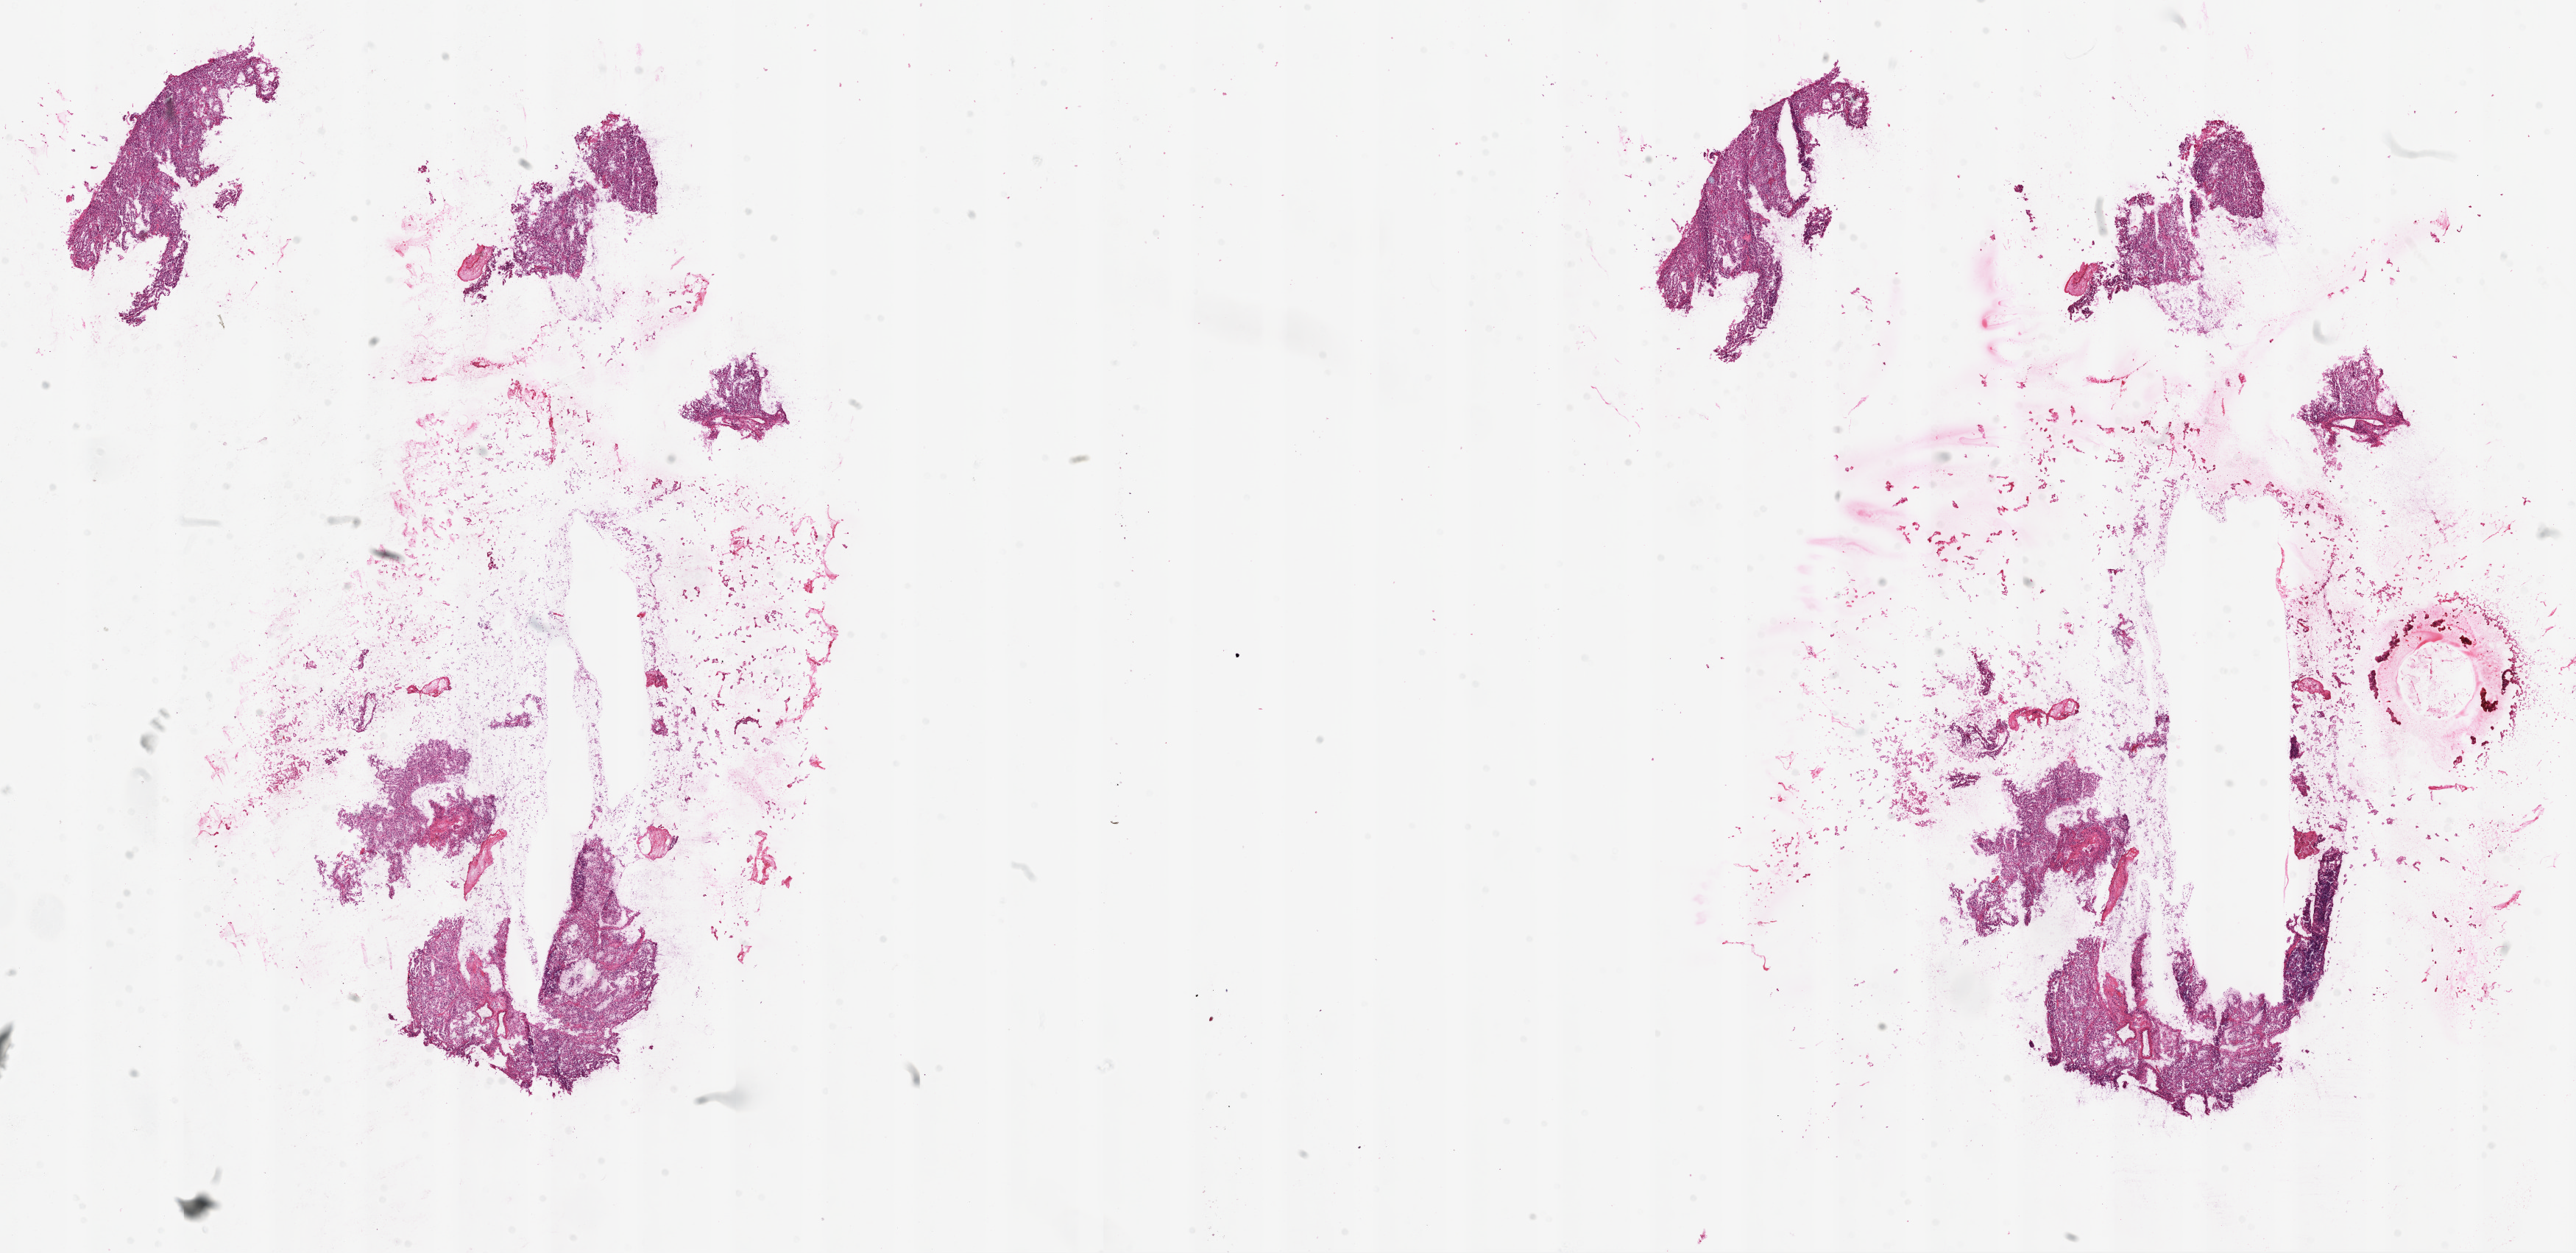
Digitized H&E tissue section (whole slide) — whole scanned area (about 28.1 x 13.7 mm) shown as a low-resolution overview. Frozen section. Primary tumour sample from the kidney. Female, age 29 years at initial diagnosis. Histologic grade: G2 (moderately differentiated). Composition of this section per pathologist review: tumour cells 90%, tumour nuclei 85%, normal cells 0%, stromal cells 10%, necrosis 0%.
AJCC pathologic stage: I. Pathologic diagnosis: Clear cell adenocarcinoma, NOS.